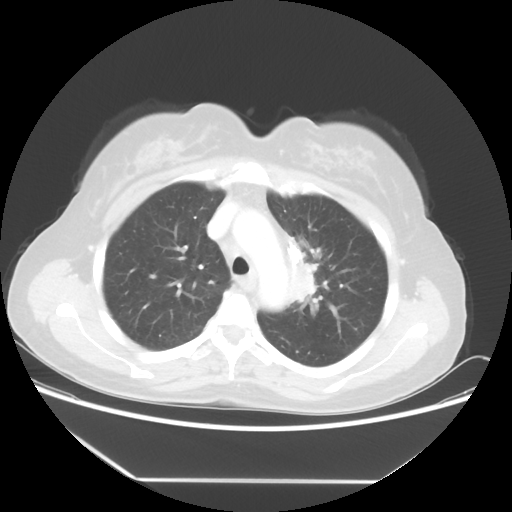
Chest CT, one axial slice. Slice 38 of 52 in the series (ordered by position). Reconstruction kernel STANDARD. Lung window (W 1500 / L -600 HU). 5 mm slice thickness. 512 × 512 image matrix, field of view 390 × 390 mm. Female patient, age 50 years. From the clinical record (not read from this slice): clinical TNM (as recorded): T2 N3 M0.
Annotated regions visible in this slice (rectangle marked by the reading radiologist):
- lung tumour (recorded histology: adenocarcinoma): bounding box <286,236,339,319> (left, top, right, bottom; pixels)